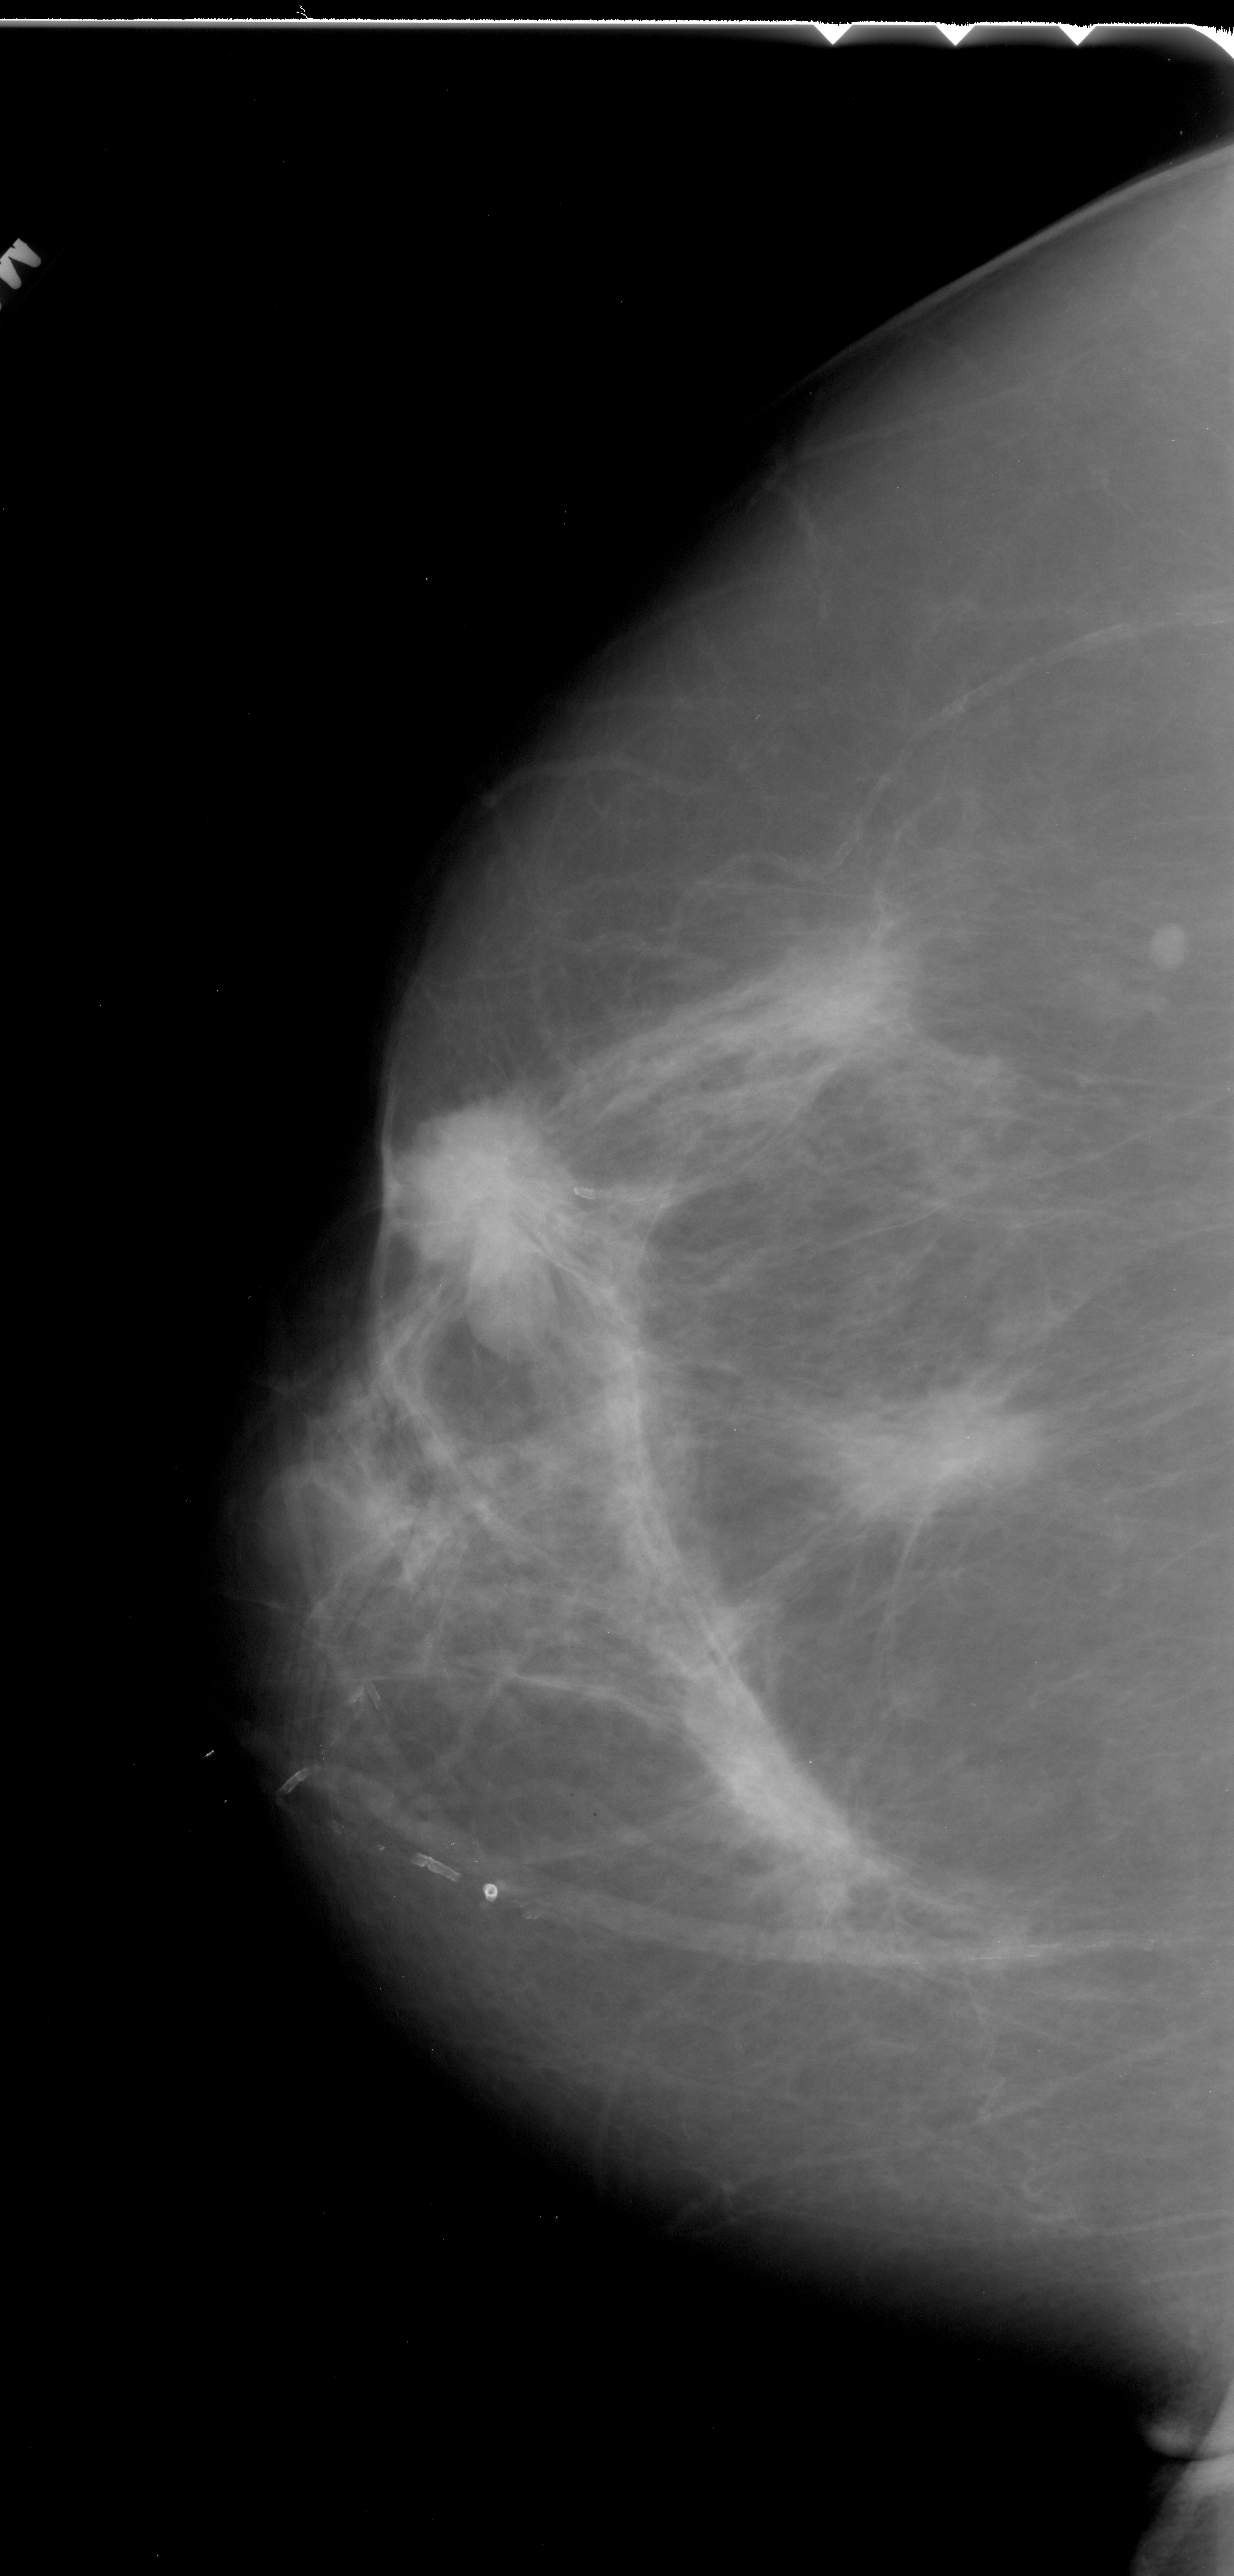
Digitized screen-film mammogram. Left breast. Craniocaudal (CC) view. BI-RADS breast density category 2 (scale 1–4). 1234 × 2576 image matrix.
Expert-marked regions of interest on this image (one box per marked abnormality):
- Finding 1 of 2: mass, shape round, margins spiculated; BI-RADS assessment category 5; pathology result (as recorded, not read from the image): malignant: box from (x=401, y=1146) to (x=584, y=1310) px
- Finding 2 of 2: mass, shape irregular, margins spiculated; BI-RADS assessment category 5; pathology result (as recorded, not read from the image): malignant: (x=869, y=1376)–(x=1056, y=1527)